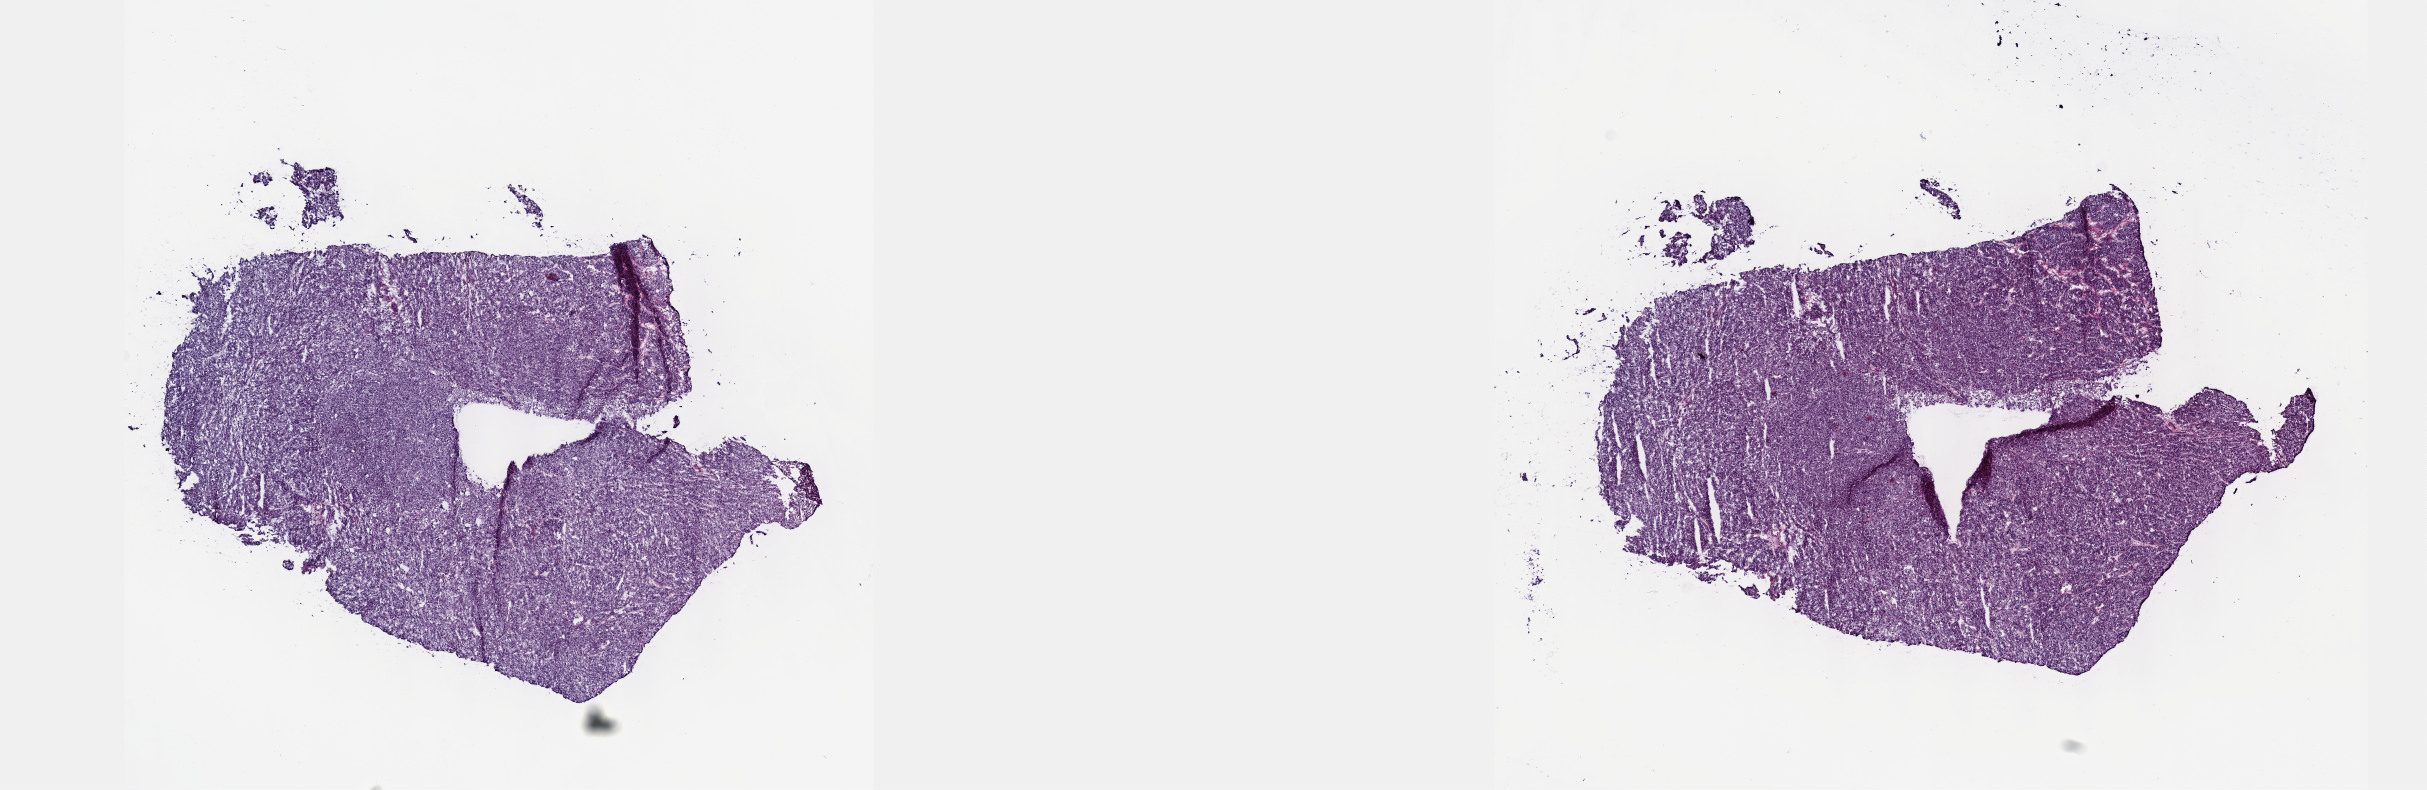
Whole-slide histology image, H&E, a low-resolution overview of the entire scanned area, about 19.6 x 6.4 mm (slide scanned at 40x); frozen section from the top of the tissue portion; sample: primary tumour, liver. Patient: female, age at initial diagnosis 43 years. Histologic grade: G2 (moderately differentiated). Slide review estimates, as recorded: tumour cells 80%, tumour nuclei 80%, normal cells 0%, stromal cells 20%, necrosis 0%. Infiltration values recorded for this section: lymphocyte infiltration 3%, monocyte infiltration 1%, neutrophil infiltration 1%.
* pathologic diagnosis: Hepatocellular carcinoma, NOS
* TNM: T1 NX MX
* AJCC pathologic stage: I (7th edition)